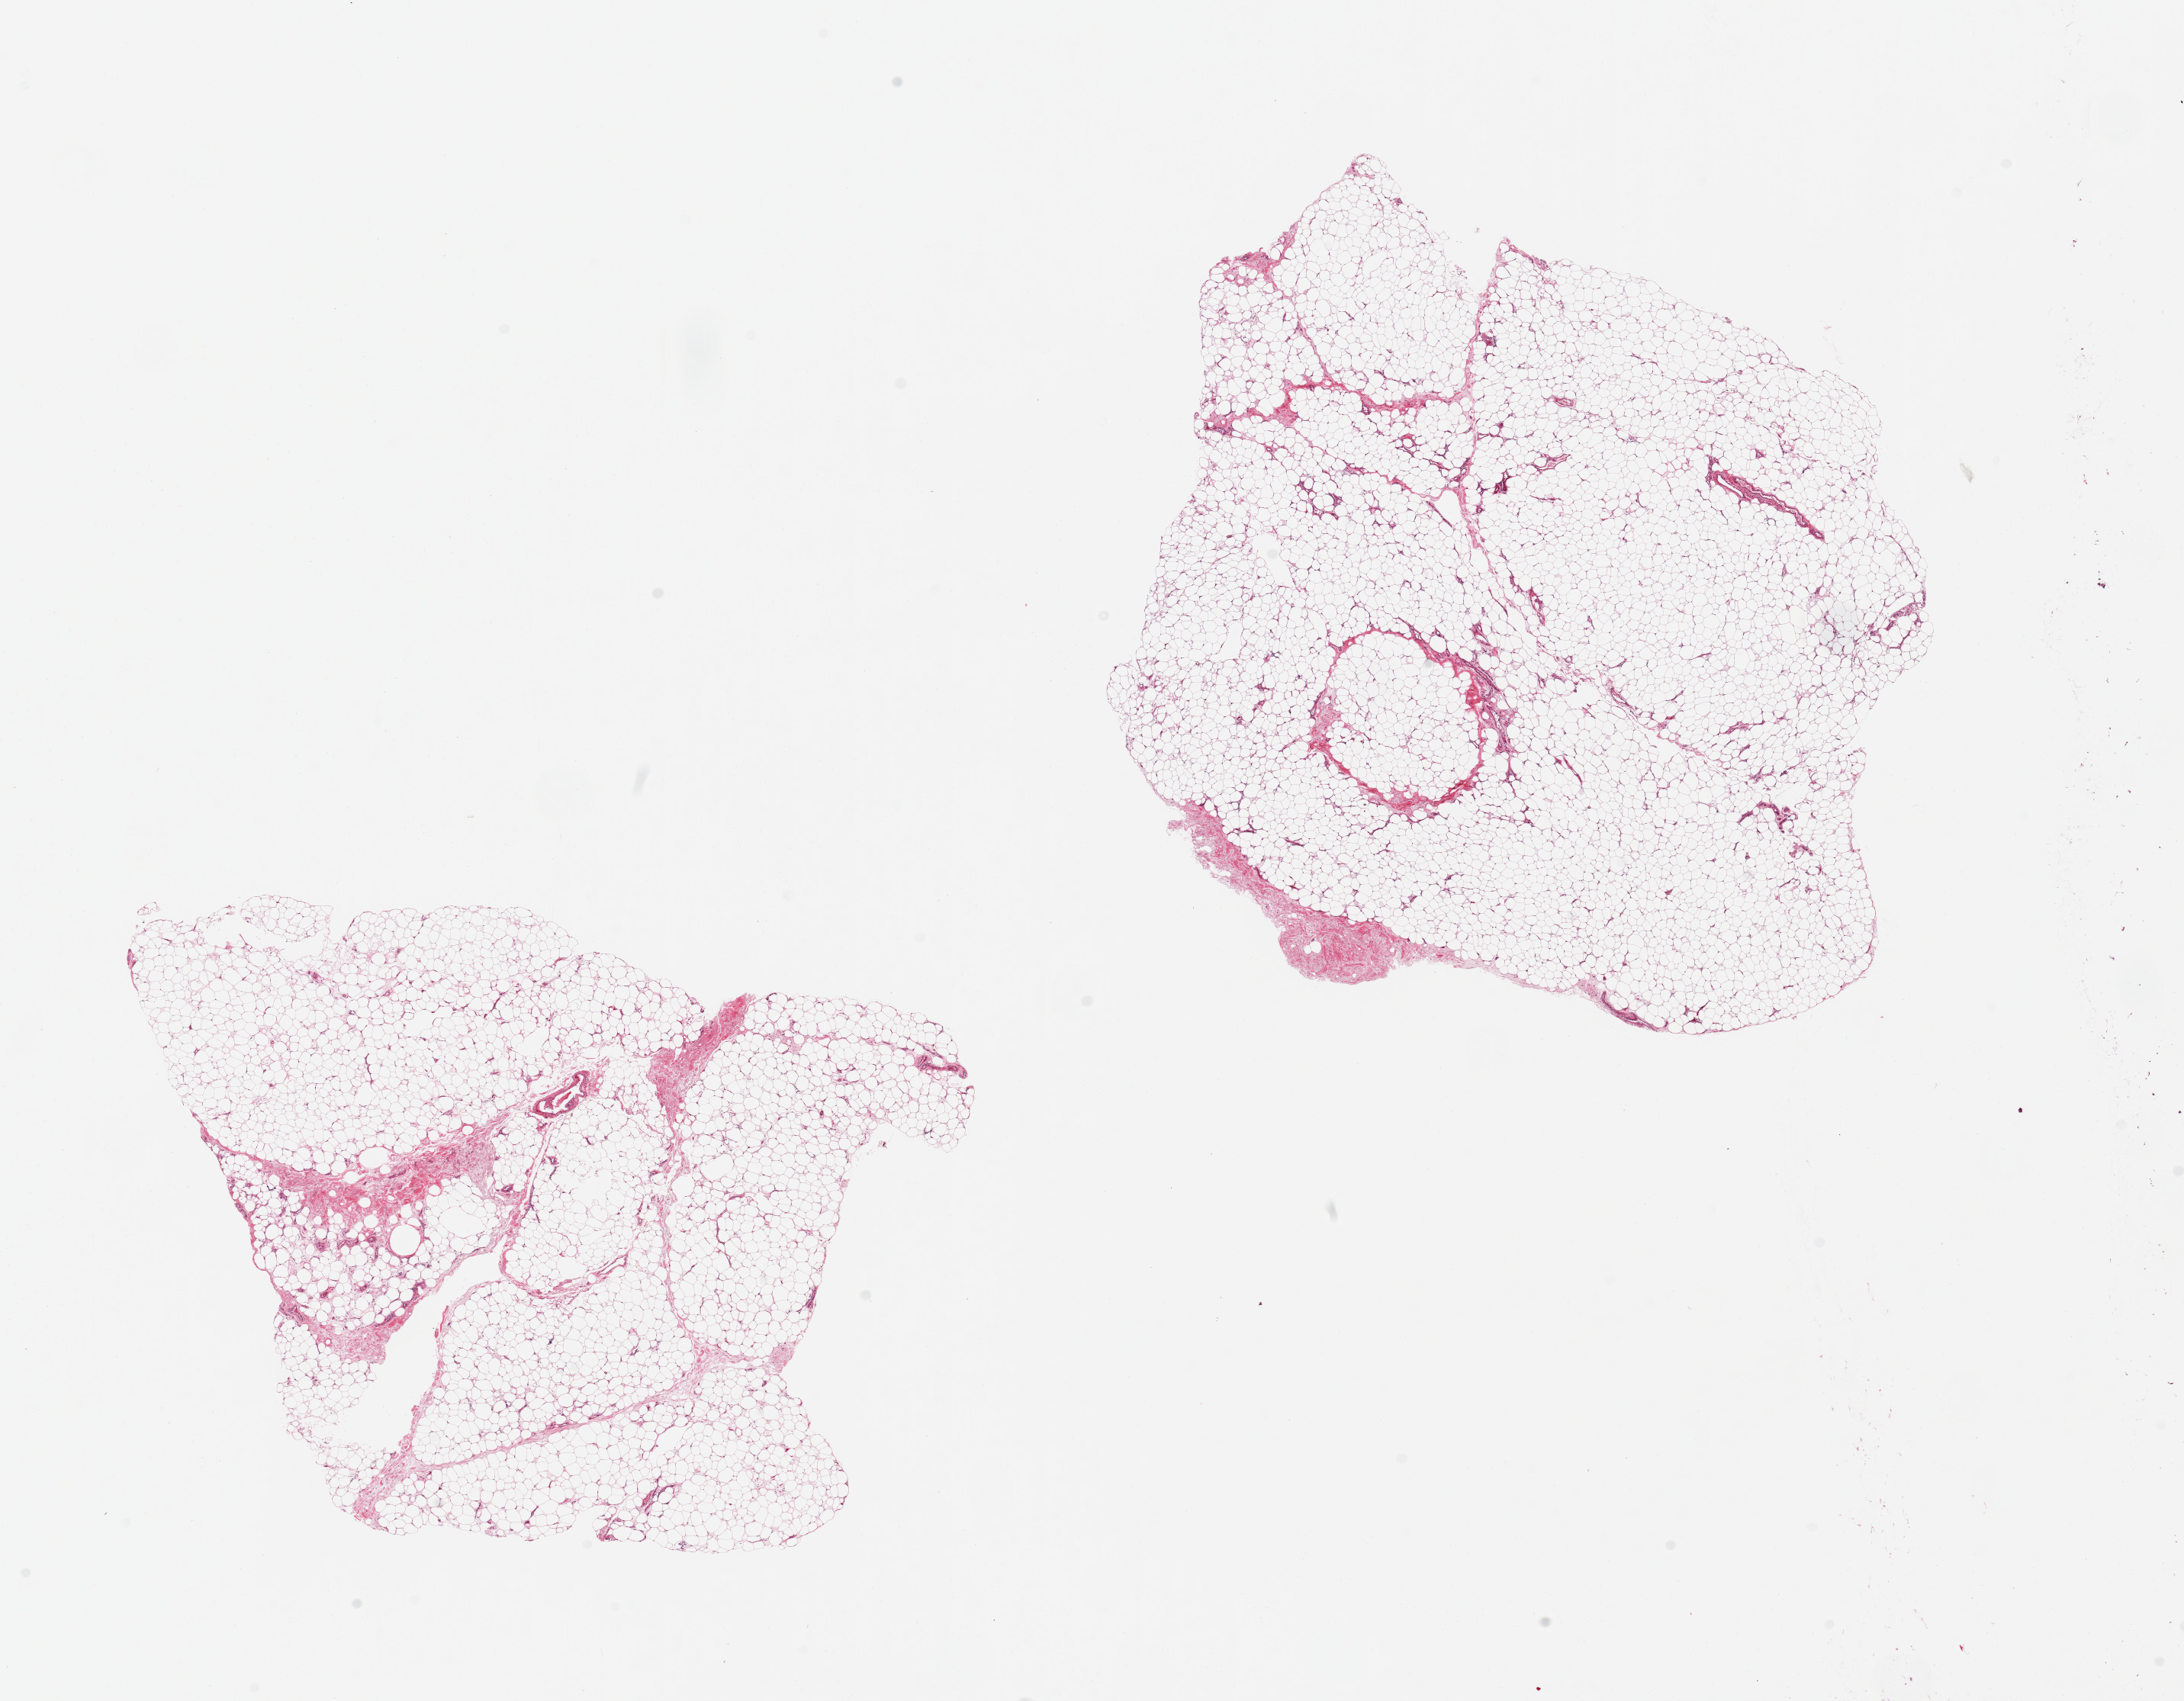
Whole-slide image, haematoxylin and eosin stain, shown as a low-resolution overview of the whole scanned area (about 22.6 x 17.6 mm, from a 20x scan), PAXgene-fixed paraffin-embedded (PFPE) section, section of adipose tissue (target tissue), donor tissue sample. Donor sex: female.
Reviewer comment on this tissue sample: 2 pieces.